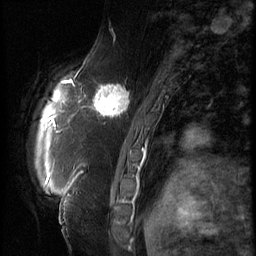
Breast MRI (dynamic contrast-enhanced), one sagittal slice; 3 images stored at this slice position (order not interpretable as contrast timing); 1.5 T; TE 4.2 ms, TR 9 ms; 256 × 256 image matrix. Female patient, age 57 years. From the clinical record (not read from this slice): setting: breast cancer imaged before/during neoadjuvant chemotherapy; receptor status: triple-negative.
Structures marked on this image (semi-automatic segmentation, software-assisted and operator-edited):
- analysis volume of interest (the breast-tissue region the enhancement analysis was run in; not a lesion): bounding box <86,74,138,129> (left, top, right, bottom; pixels)
- tumour enhancement mask (voxels above the 140 % enhancement threshold inside the analysis volume of interest): <86,84,131,118>